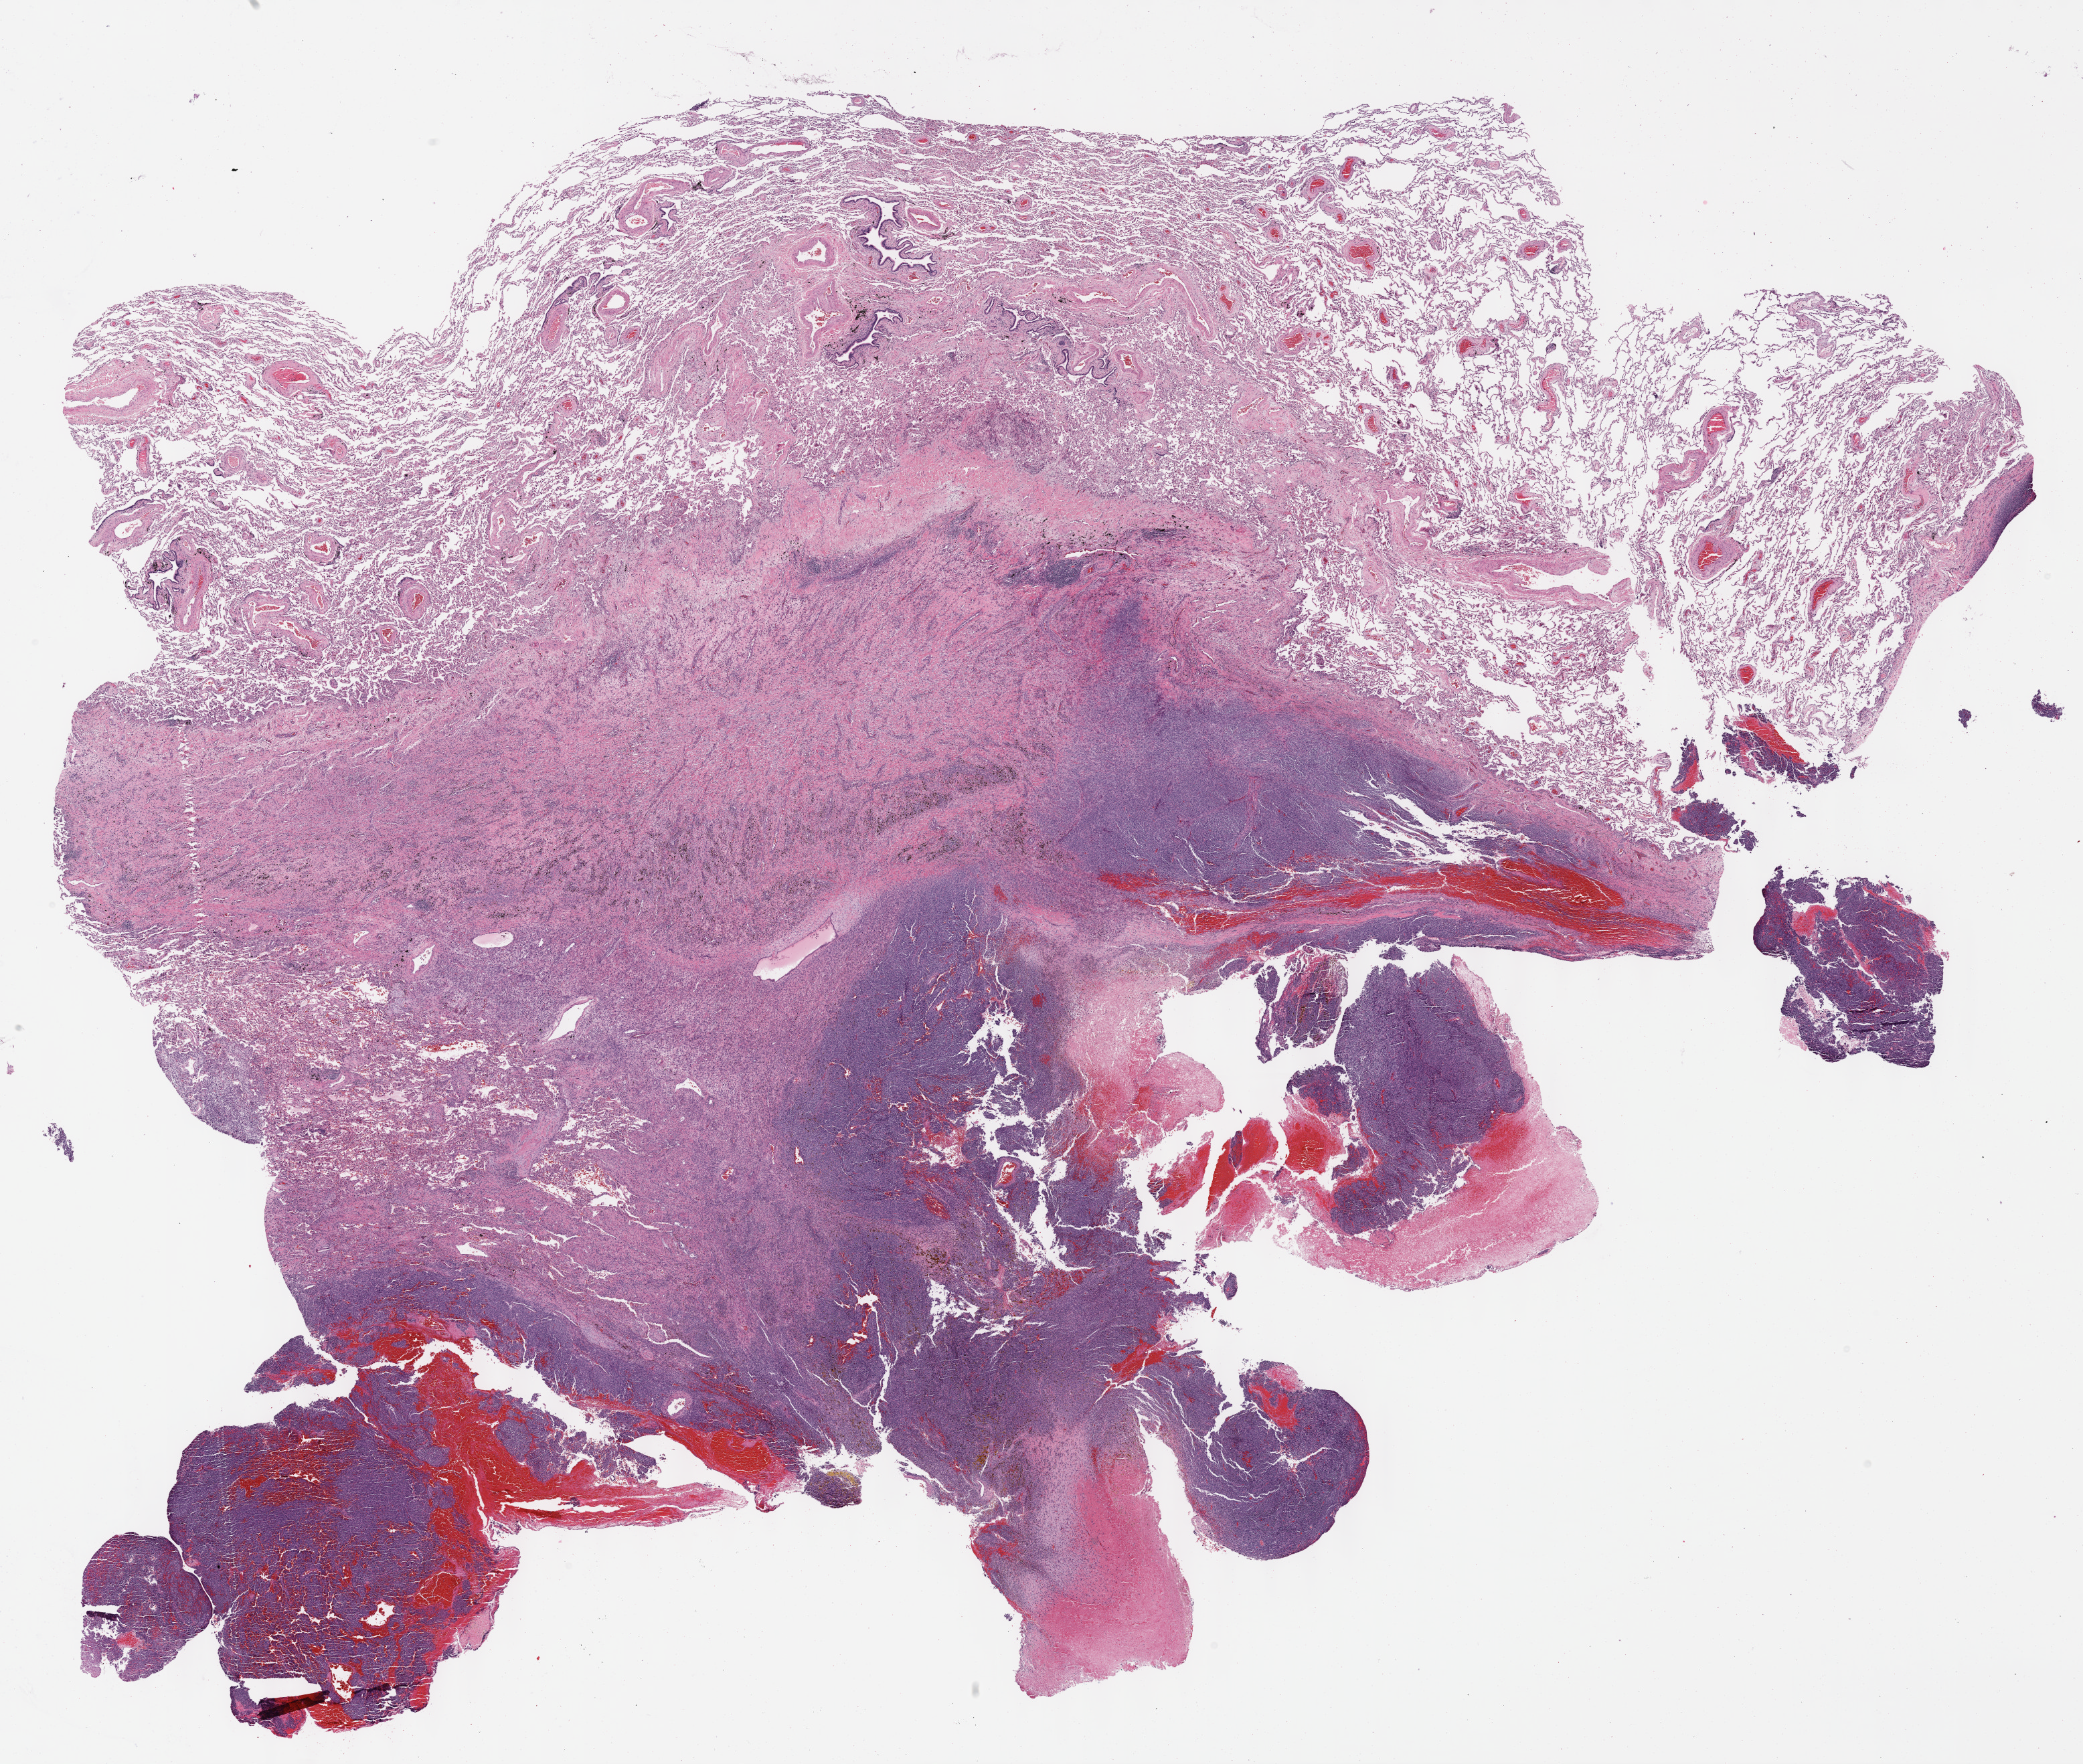
Digitized H&E-stained tissue section (whole slide) — a low-resolution overview of the entire scanned area, about 25.1 x 21.3 mm (from a 40x scan); formalin-fixed paraffin-embedded (FFPE) diagnostic section; connective, subcutaneous and other soft tissues, primary tumour sample. Patient: male, age at initial diagnosis 69 years.
Pathologic diagnosis: Synovial sarcoma, spindle cell (connective, subcutaneous and other soft tissues of thorax).